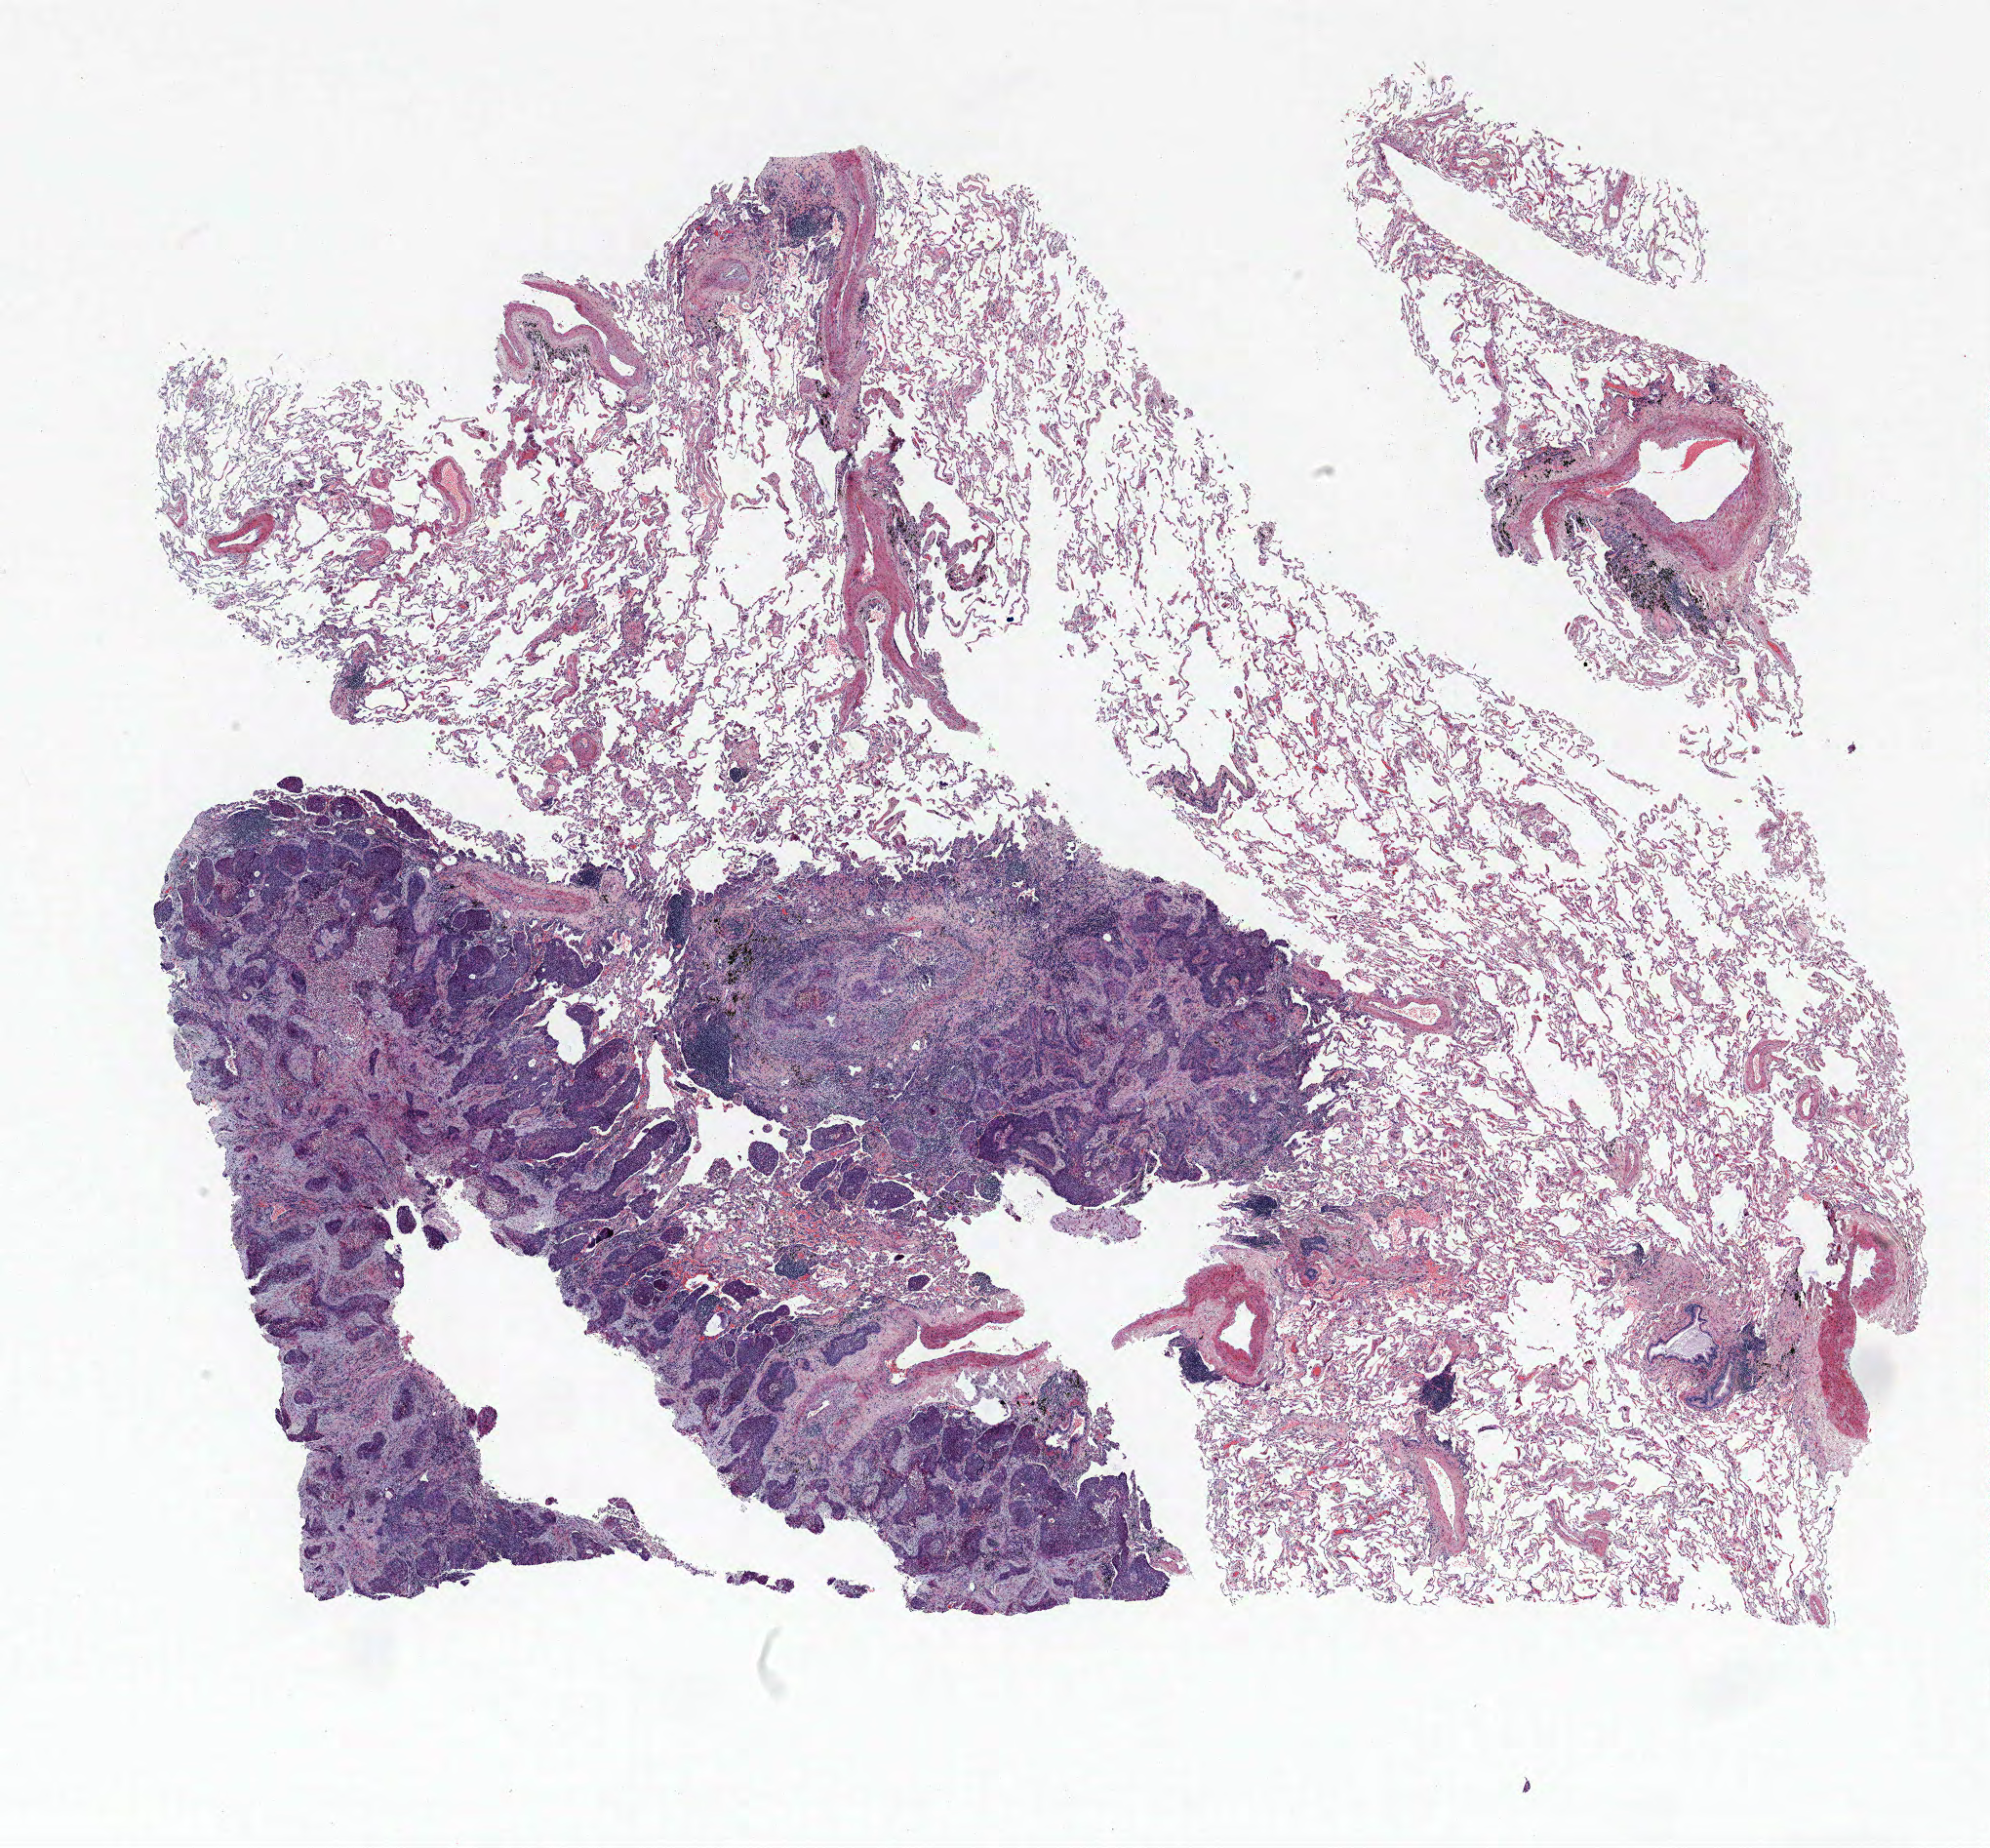
H&E whole-slide image — shown as a low-resolution overview of the whole scanned area (about 16.3 x 15.2 mm, acquisition: 40x scan); FFPE section; lung tissue. Male, age 70 at enrolment. Former smoker at enrolment. Grade: poorly differentiated (G3).
* participant's lung-cancer diagnosis: Squamous cell carcinoma, NOS (ICD-O-3 8070/3)
* tumour size (pathology): 18 mm
* stage (AJCC 6th edition): IA
* primary tumour location (clinical record): right upper lobe